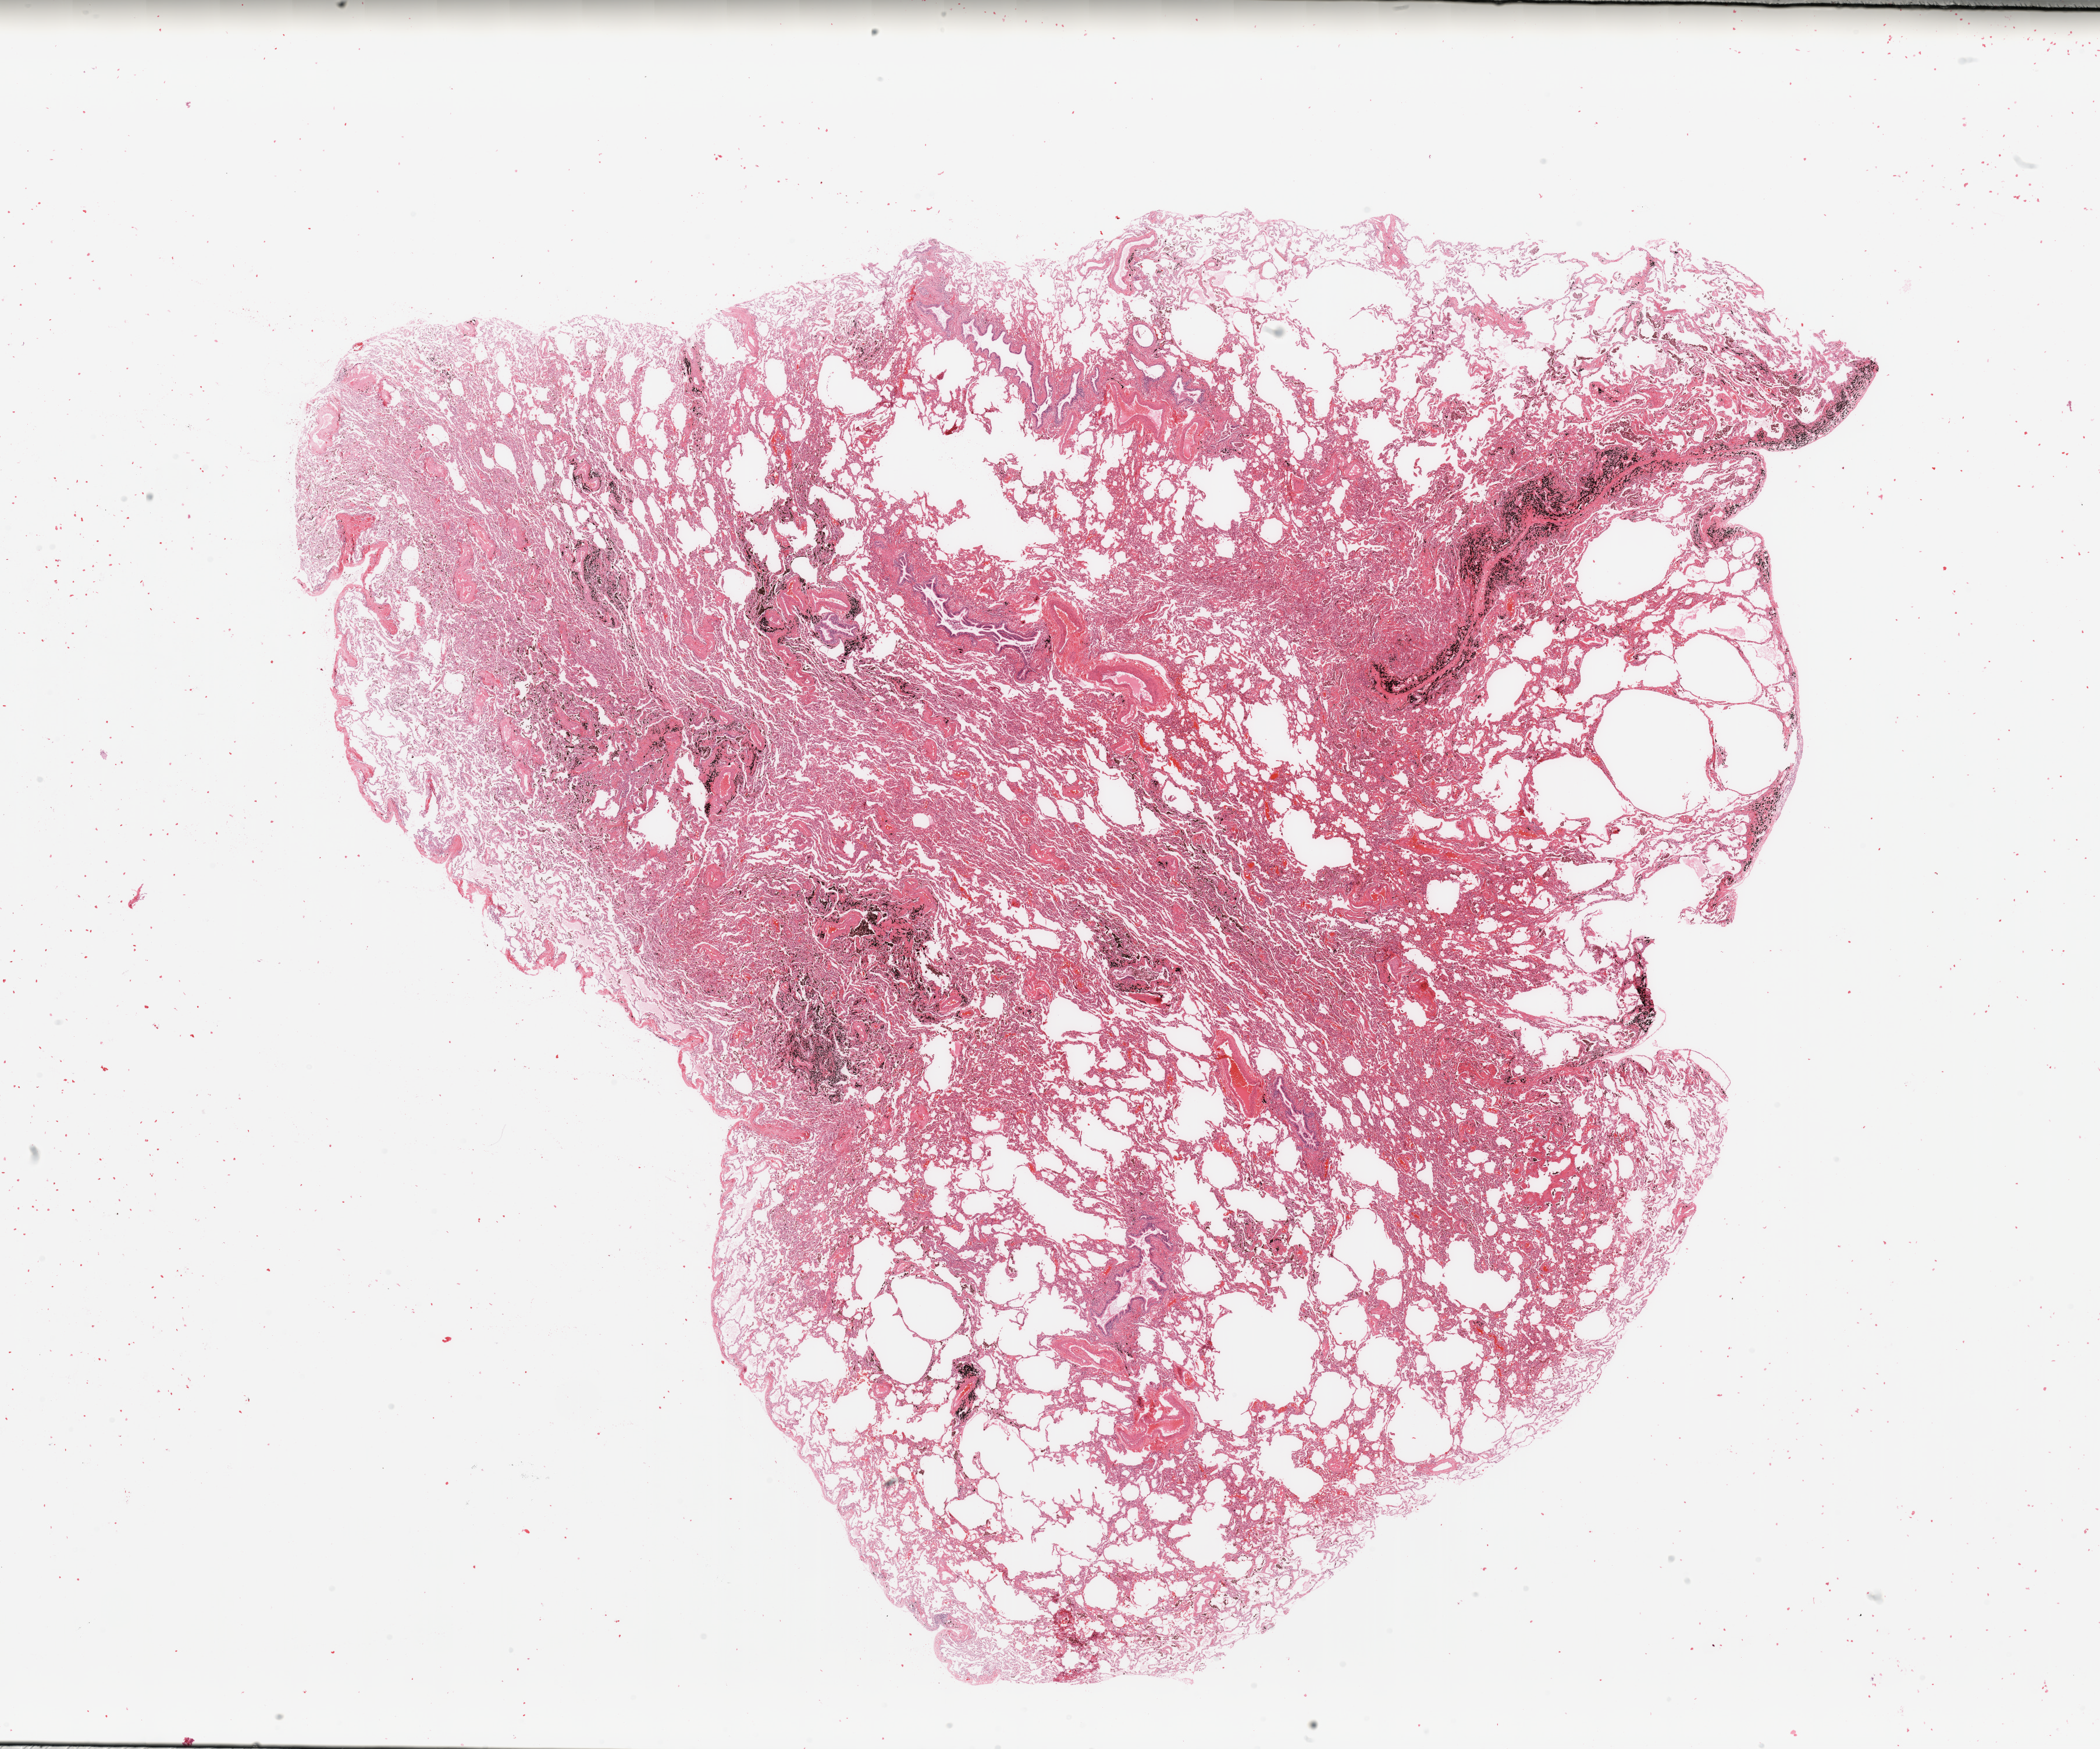
H&E whole-slide image, whole scanned area (about 28.5 x 23.8 mm) shown as a low-resolution overview; normal (non-tumour) tissue sample, sampled site: lung. Male, 64 y/o.
This section: normal (non-tumour) tissue from the same patient. Patient diagnosis: Adenocarcinoma, NOS.